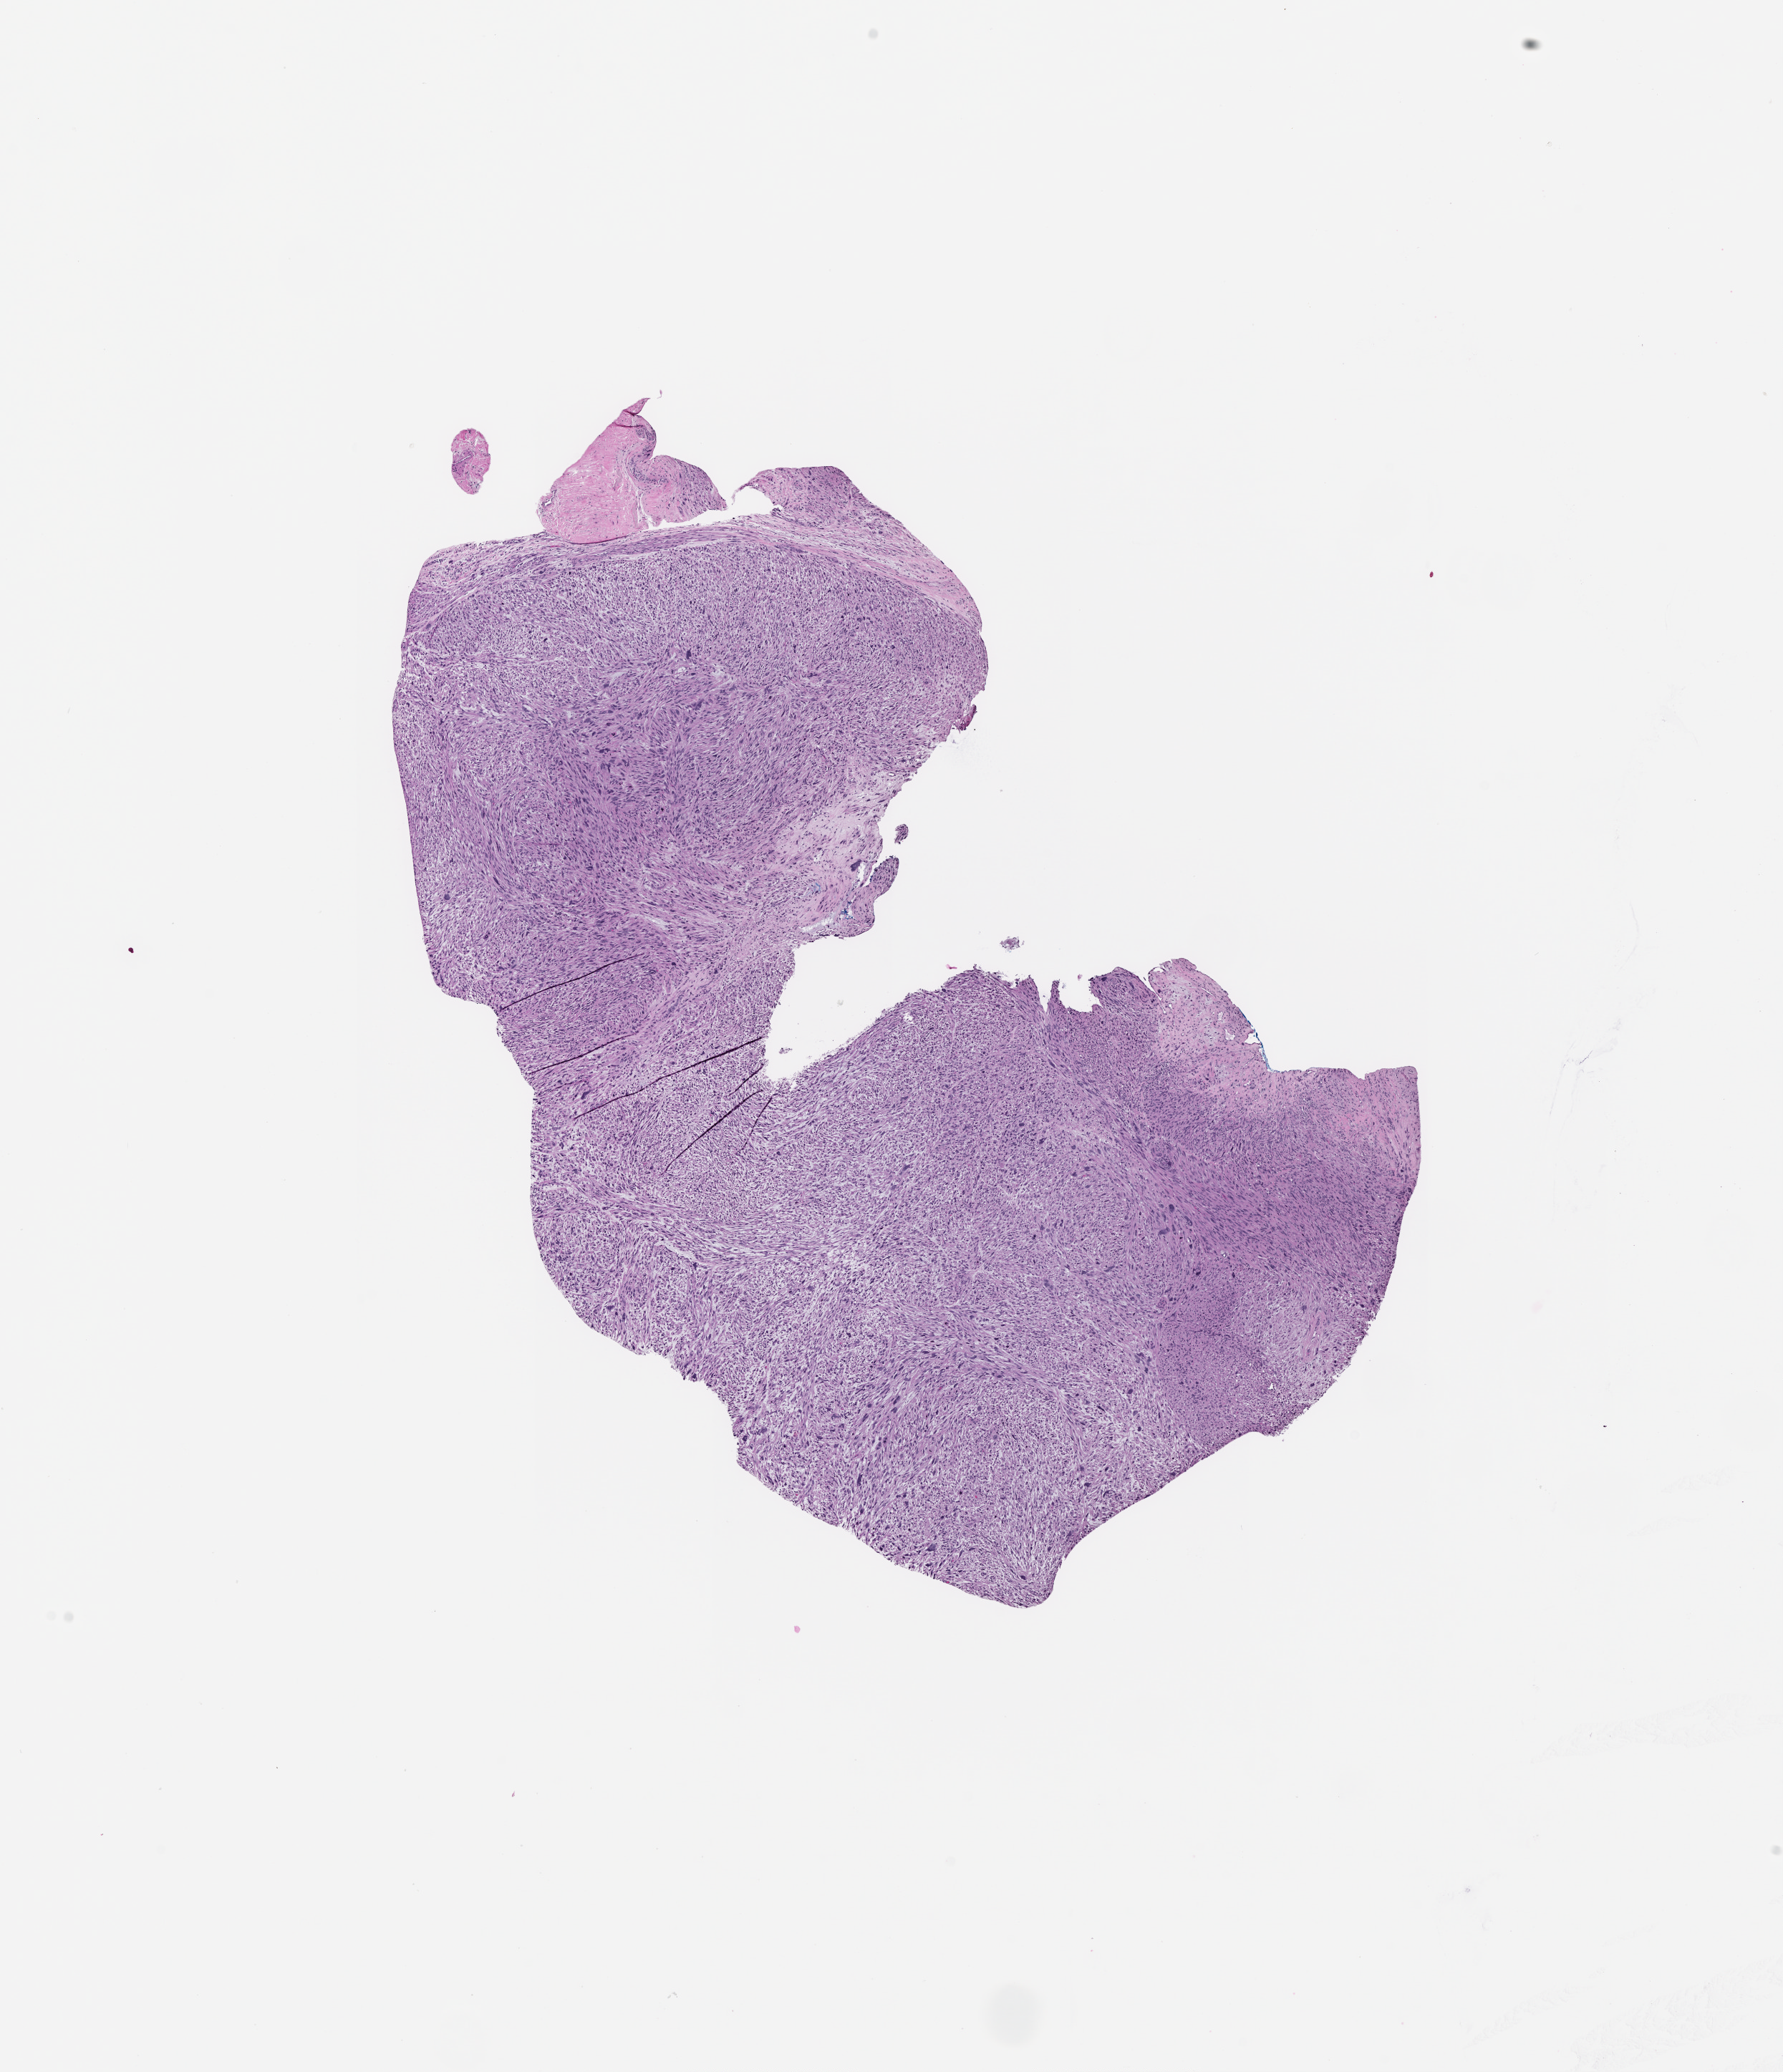
Digitized H&E tissue section (whole slide), whole scanned area (about 10.0 x 11.6 mm) shown as a low-resolution overview.
Patient diagnosis (cohort enrolment): sarcoma (site not recorded at cohort level).